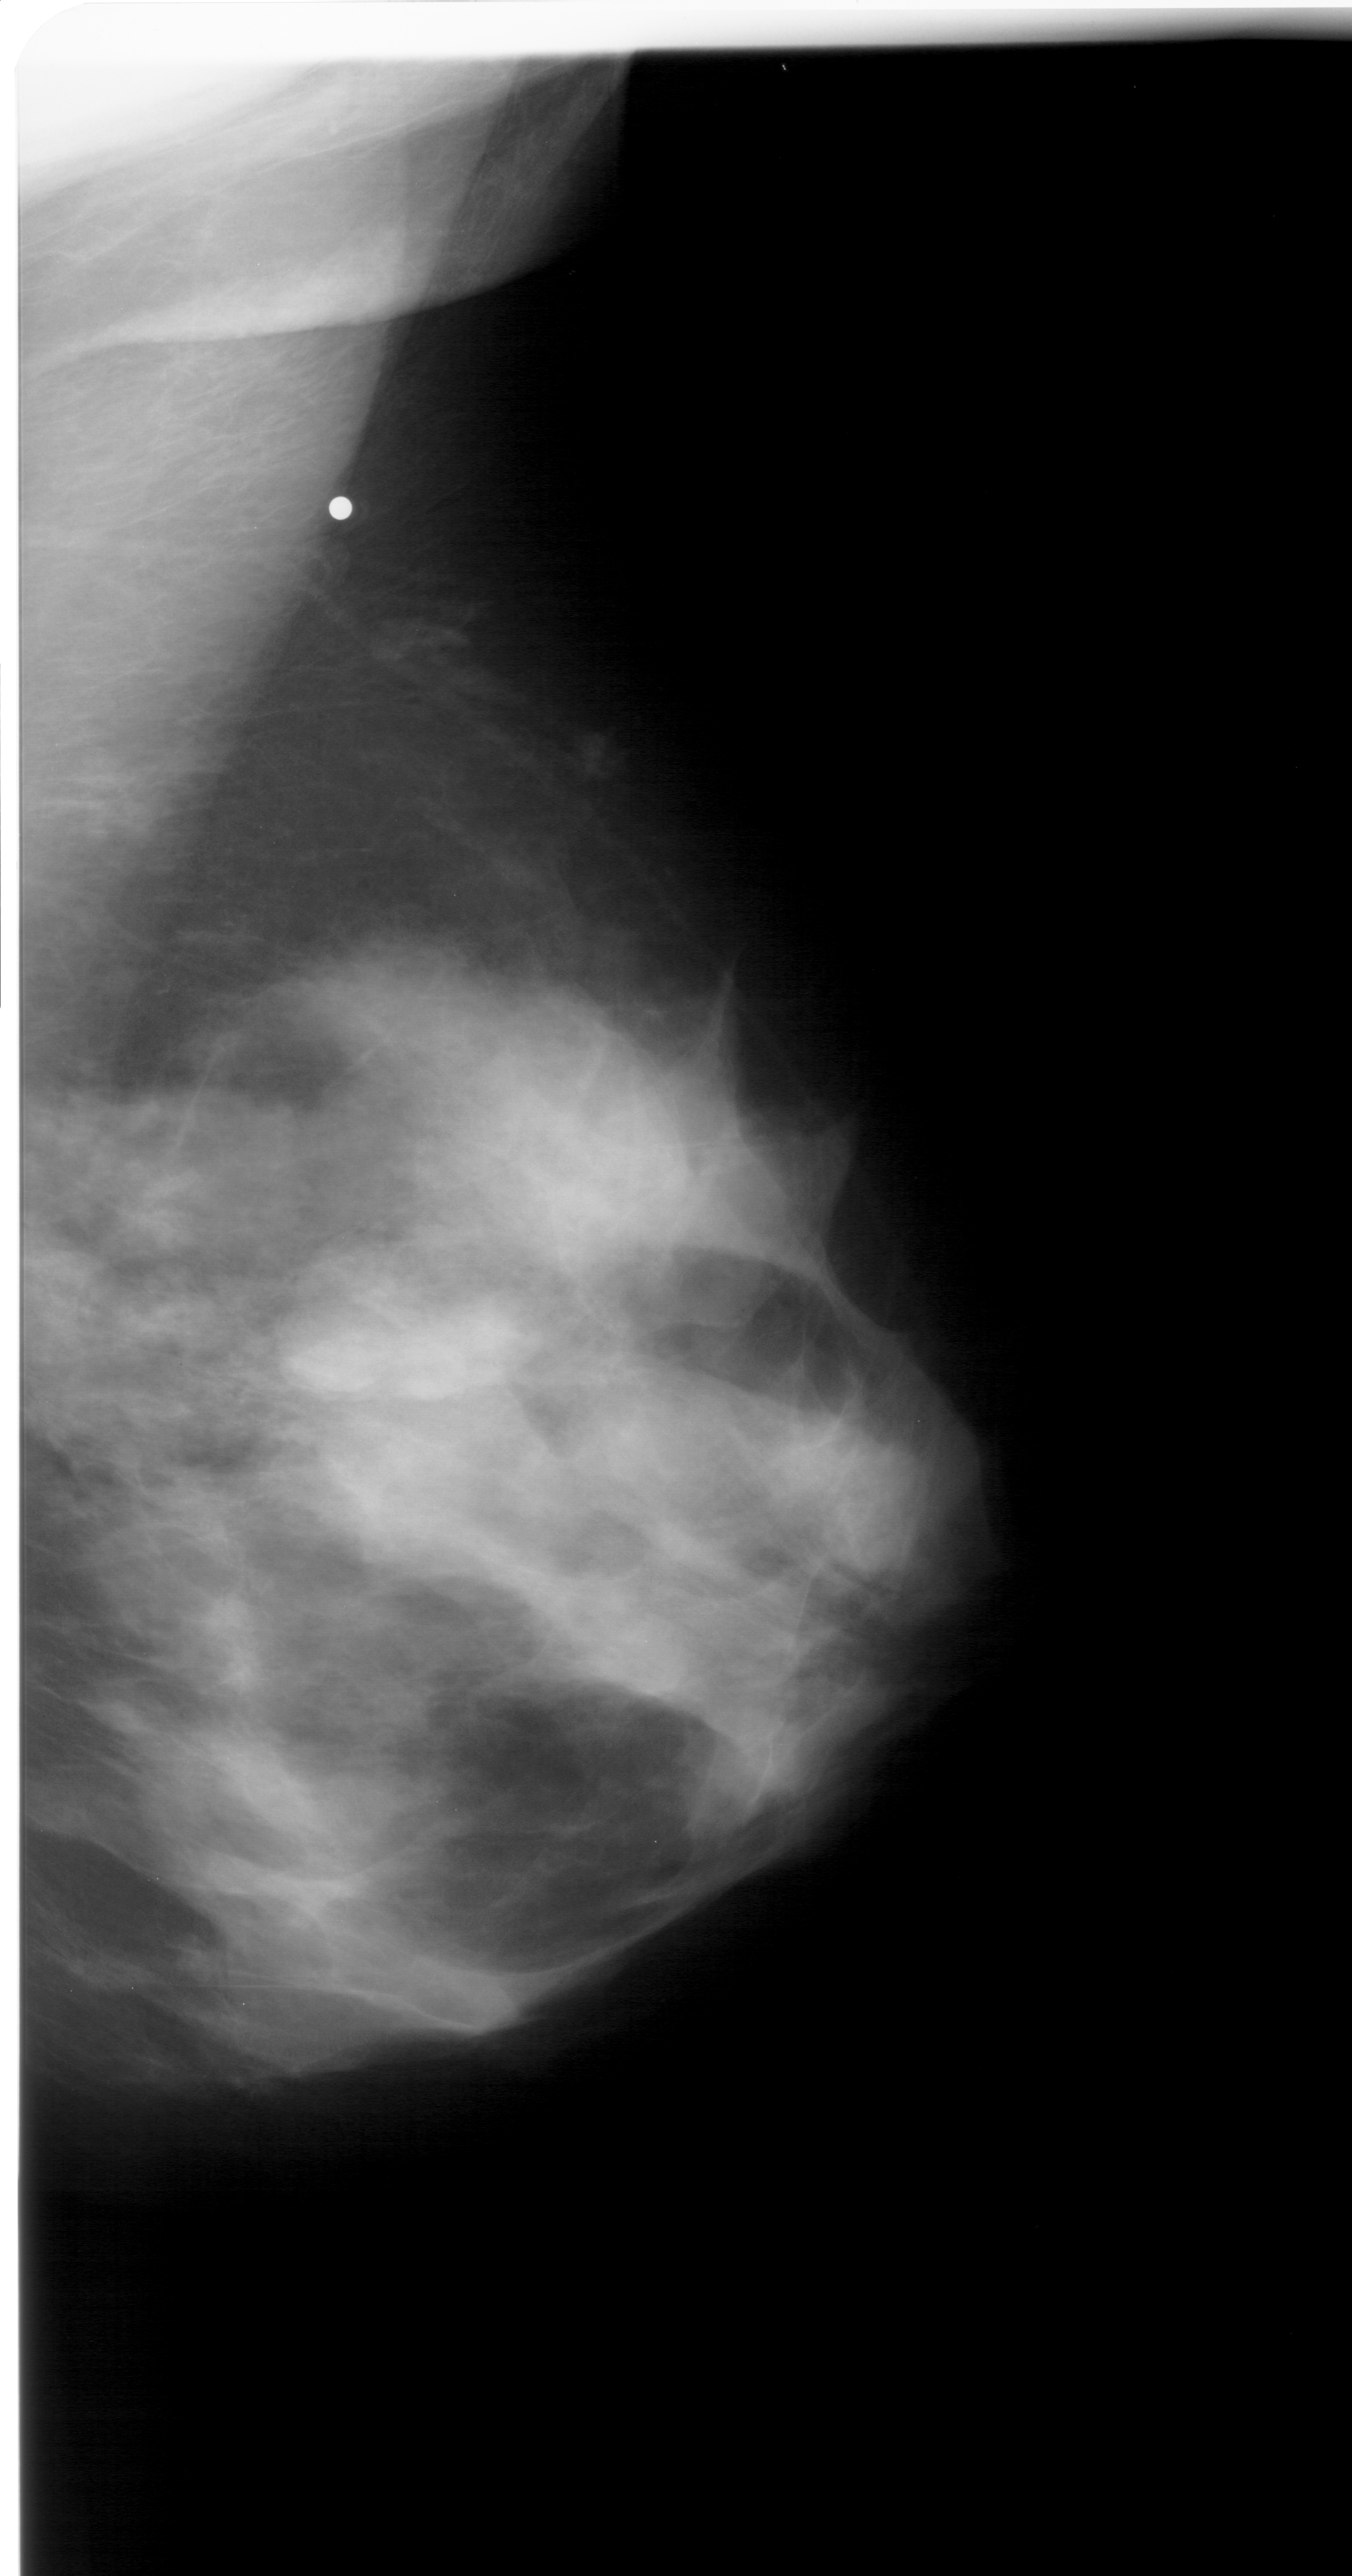
Digitized screen-film mammogram; right breast; mediolateral oblique (MLO) view; breast composition: extremely dense (BI-RADS density category 4 of 4).
- Abnormality record for this image: mass, shape lobulated, margins obscured; BI-RADS assessment category 4; pathology (as recorded): benign.